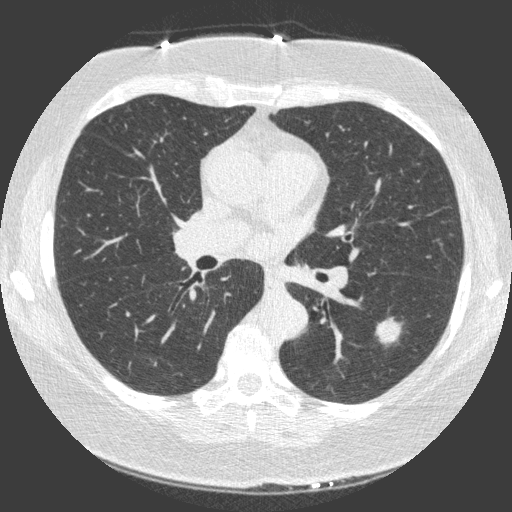
Low-dose screening chest CT, one axial slice; position 89 of 149 along the scan axis; lung window (W 1500 / L -600 HU); 512 × 512 image matrix, field of view 330 × 330 mm.
Annotated regions visible in this slice (expert manual segmentation):
- lesion 1 (tumor, lower lobe of left lung): bounding box (x1, y1, x2, y2) in pixels: (376, 318, 401, 344)